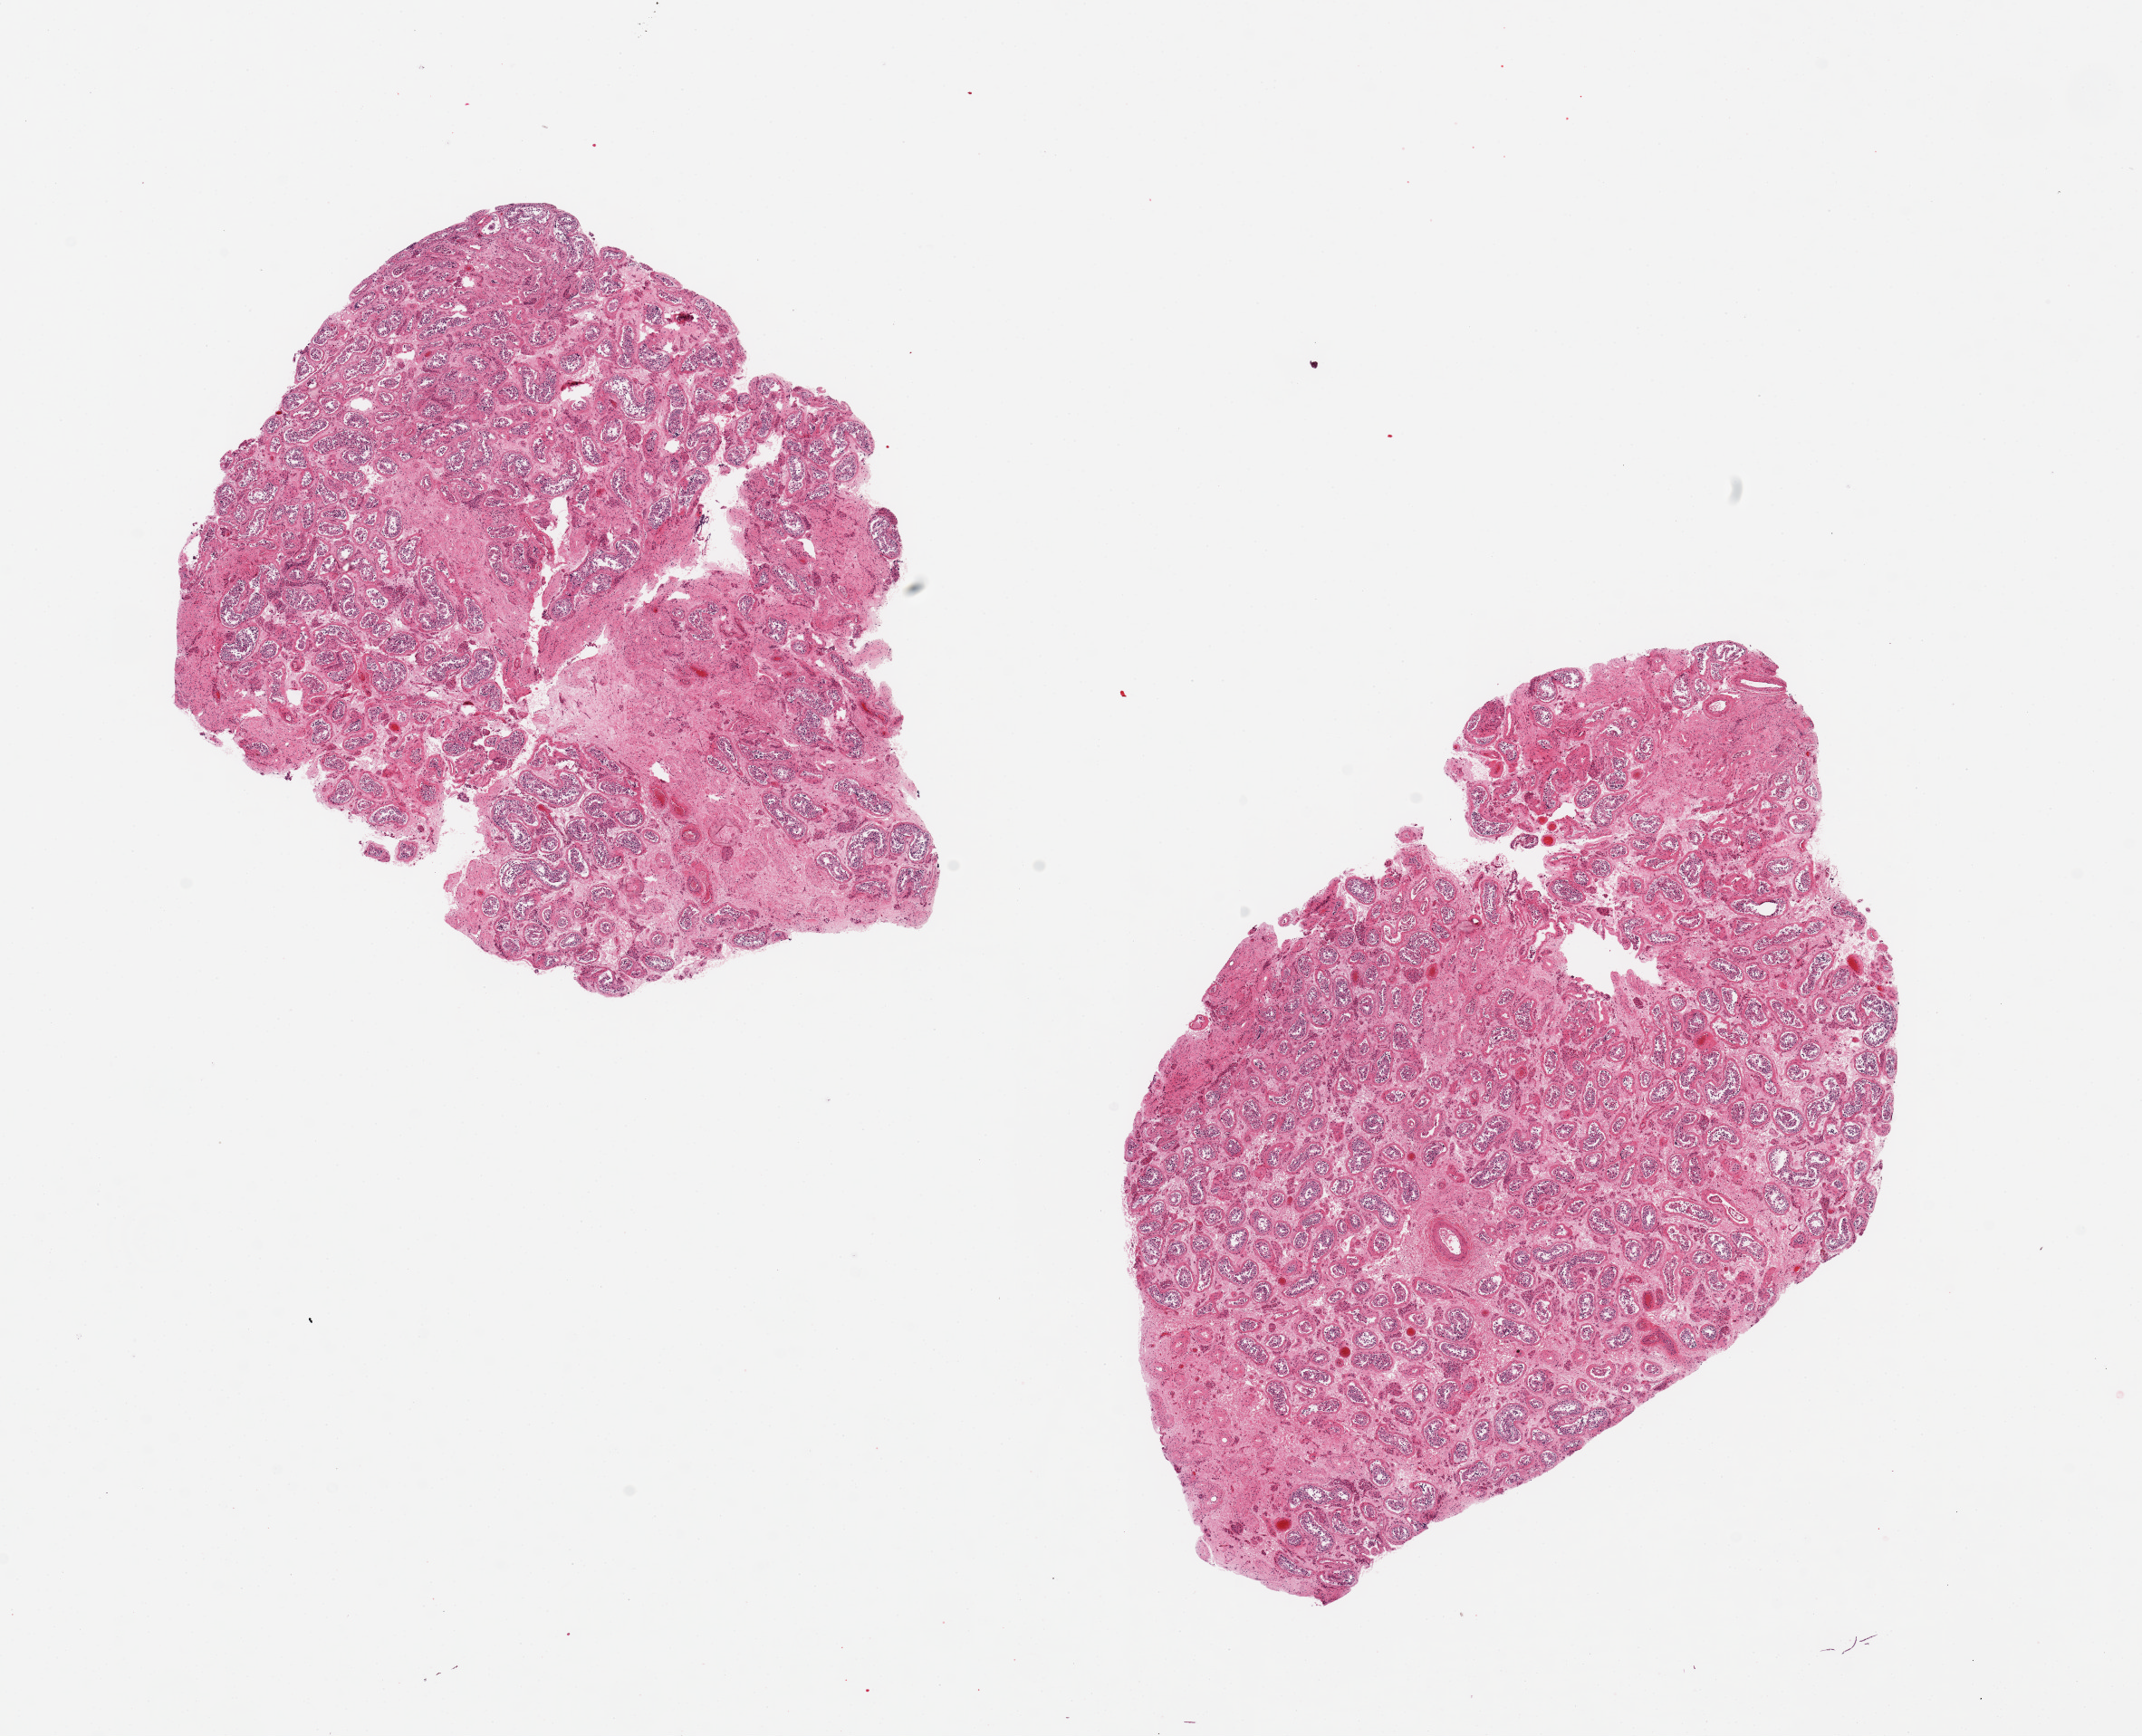
Digitized hematoxylin and eosin (H&E)-stained section — shown as a low-resolution overview of the whole scanned area (about 18.7 x 15.2 mm); PAXgene-fixed, paraffin-embedded tissue; section of testis (target tissue); tissue donor sample. Donor: male.
- pathologist's review note for this sample: 2pieces ~ 8x6mm, marked tubular atrophy, reduce spermatogenesis, but badly autolyzed